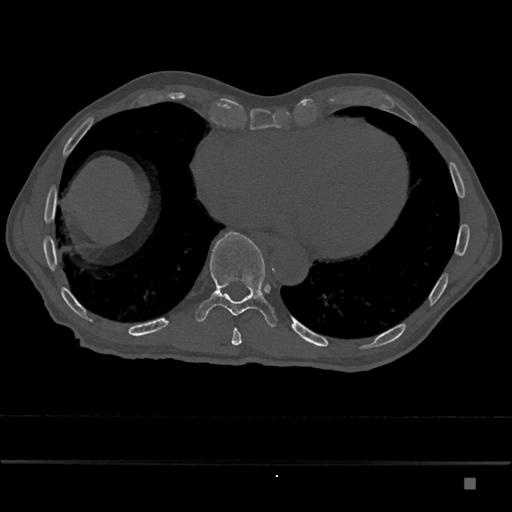
CT including the spine, one axial slice. Slice 748 of 797 in the series (ordered by position). Reconstruction kernel Br40s/3. 120 kVp. Bone window (W 1800 / L 400 HU). 512 × 512 image matrix. Male patient, age 72 years. From the clinical record (not read from this slice): primary cancer: prostate.
Structures marked on this image (semi-automatic segmentation, software-assisted and operator-edited):
- T10 vertebra: bounding box (x1, y1, x2, y2) in pixels: (195, 231, 278, 327)
- T9 vertebra: (231, 328, 242, 346)